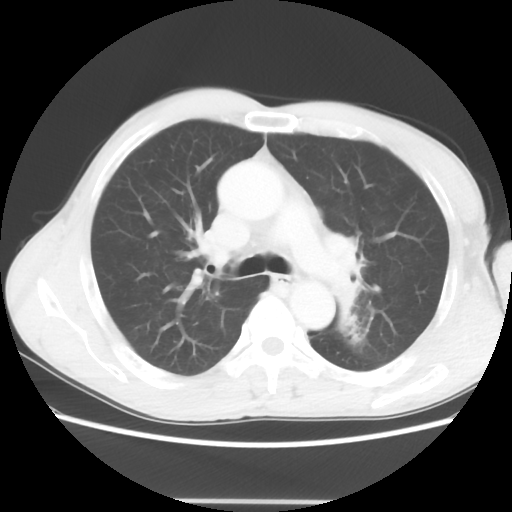
Chest CT, one axial slice; slice 42 of 62 in the series (ordered by position); reconstruction kernel STANDARD; 100 kVp; lung window (W 1500 / L -600 HU); 5 mm slice thickness; 512 × 512 image matrix. Patient: male, 61 years. Case-level facts recorded for this patient, not image findings: clinical TNM (as recorded): T3 N1 M1.
Outlined on this slice (rectangle marked by the reading radiologist):
- lung tumour (recorded histology: adenocarcinoma): bounding box (x1, y1, x2, y2) in pixels: (323, 224, 366, 326)